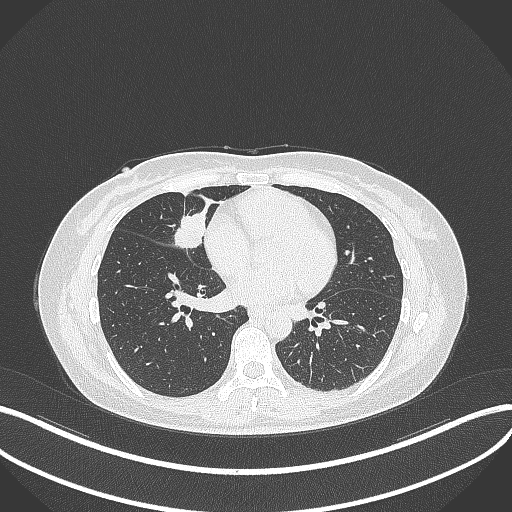
Chest CT, one axial slice. Position 122 of 284 along the scan axis. Reconstruction kernel B70f. 120 kVp. Lung window (W 1500 / L -600 HU). 1 mm slice thickness. 512 × 512 image matrix, field of view 400 × 400 mm. Patient: female, 43 years. Case-level facts recorded for this patient, not image findings: clinical TNM (as recorded): T1c N3 M1.
Structures marked on this image (rectangle marked by the reading radiologist):
- lung tumour (recorded histology: adenocarcinoma): bounding box [x1, y1, x2, y2] px = [172, 207, 207, 257]